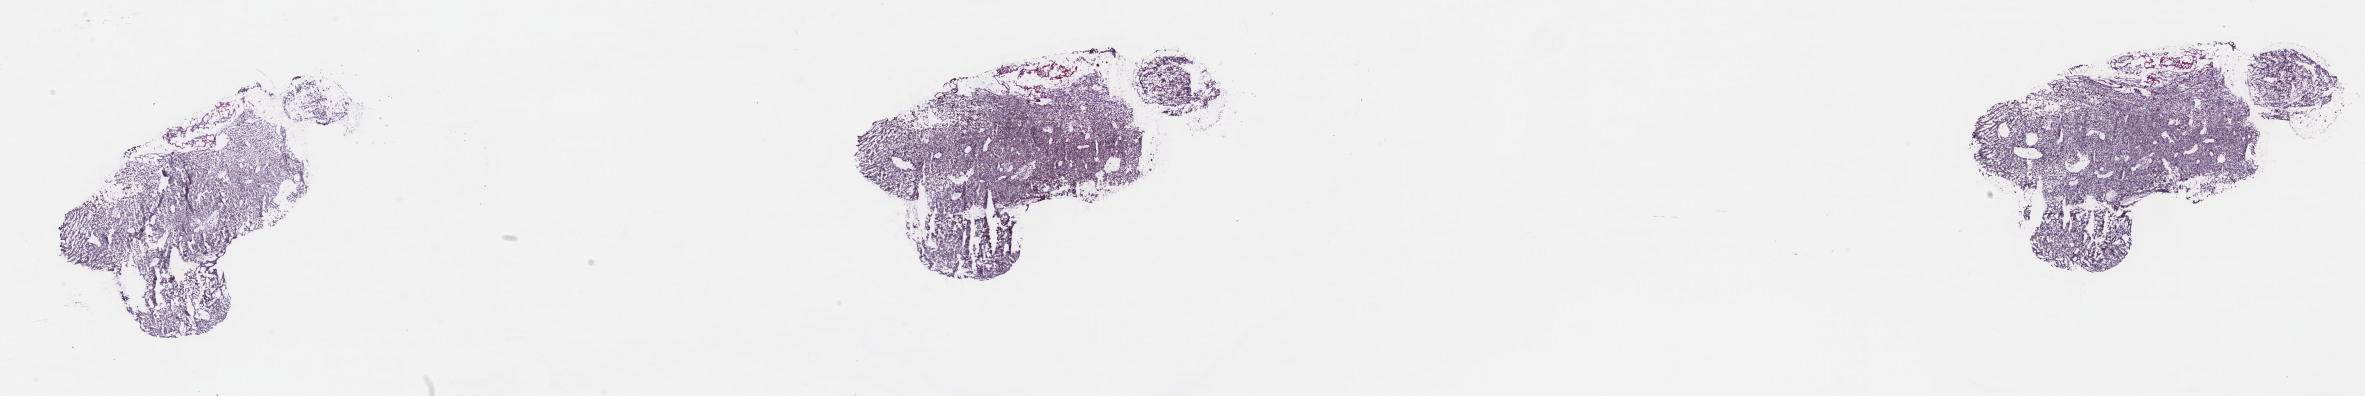
H&E-stained whole-slide image — shown as a low-resolution overview of the whole scanned area (about 38.3 x 6.4 mm, from a 40x scan); frozen section from the top of the tissue portion; sample: primary tumour, uvea. Patient: female, age at initial diagnosis 50 years. Composition of this section per pathologist review: tumour cells 90%, tumour nuclei 90%, normal cells 0%, stromal cells 10%, necrosis 0%. Infiltration values recorded for this section: lymphocyte infiltration 0%, monocyte infiltration 0%, neutrophil infiltration 0%.
* AJCC pathologic stage: IIB (7th edition)
* laterality: right
* histologic diagnosis: Spindle cell melanoma, NOS (overlapping lesion of eye and adnexa)